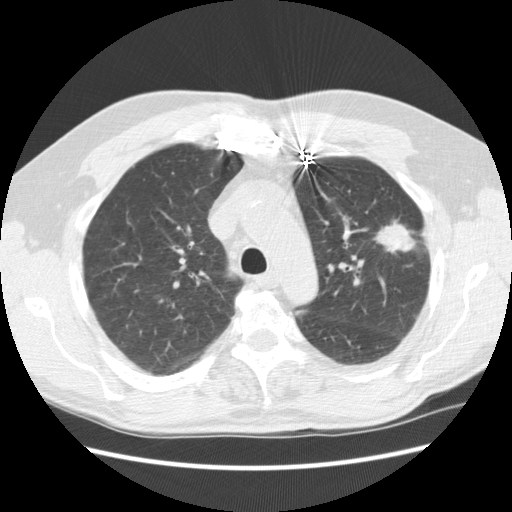
Low-dose screening chest CT, axial slice, baseline screening round, lung window (W 1500 / L -600 HU), 2.5 mm slice thickness, standard (soft-tissue) reconstruction kernel (STANDARD), slice 175 of 231 in the series, 512 × 512 image matrix. Male participant, aged 72 years at enrolment. Former smoker at enrolment.
Lesion marked by an expert reader, bounding box [x1, y1, x2, y2] px = [350, 200, 429, 260]. The exam's reader record, not a measurement of the box and not confirmed to be the same lesion: non-calcified nodule or mass ≥4 mm, left upper lobe, 25 × 18 mm, spiculated (stellate) margins, soft tissue attenuation. Official screen result: positive, change unspecified: nodule(s) >= 4 mm or enlarging nodule(s), mass(es), or other non-specific abnormalities suspicious for lung cancer. Later outcome: lung cancer diagnosed 35 days after this screen — adenocarcinoma, NOS, left upper lobe, well differentiated (G1), stage IIIB (AJCC 6th edition), 25 mm at pathology.